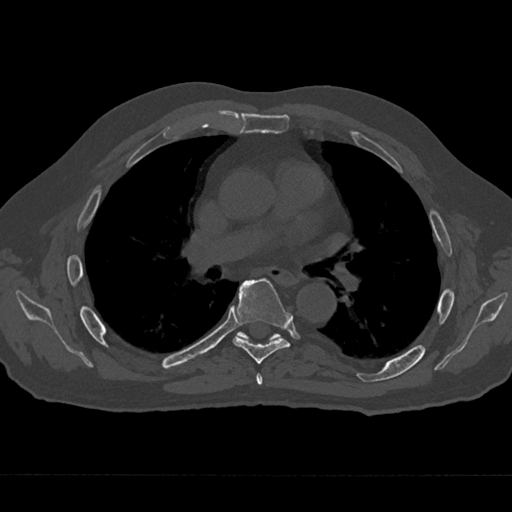
CT including the spine, one axial slice; slice 412 of 797 in the series (ordered by position); reconstruction kernel Br40s/3; 120 kVp; bone window (W 1800 / L 400 HU); 0.5 mm slice thickness; 512 × 512 image matrix, field of view 377 × 377 mm. Patient: male, 75 years. Case-level facts recorded for this patient, not image findings: primary cancer: renal; vertebrae with lytic lesions (as recorded): T4.
Structures marked on this image (semi-automatic segmentation, software-assisted and operator-edited):
- T5 vertebra: bounding box (x1, y1, x2, y2) in pixels: (256, 373, 263, 385)
- T6 vertebra: (233, 278, 291, 364)
- T7 vertebra: (238, 332, 279, 340)